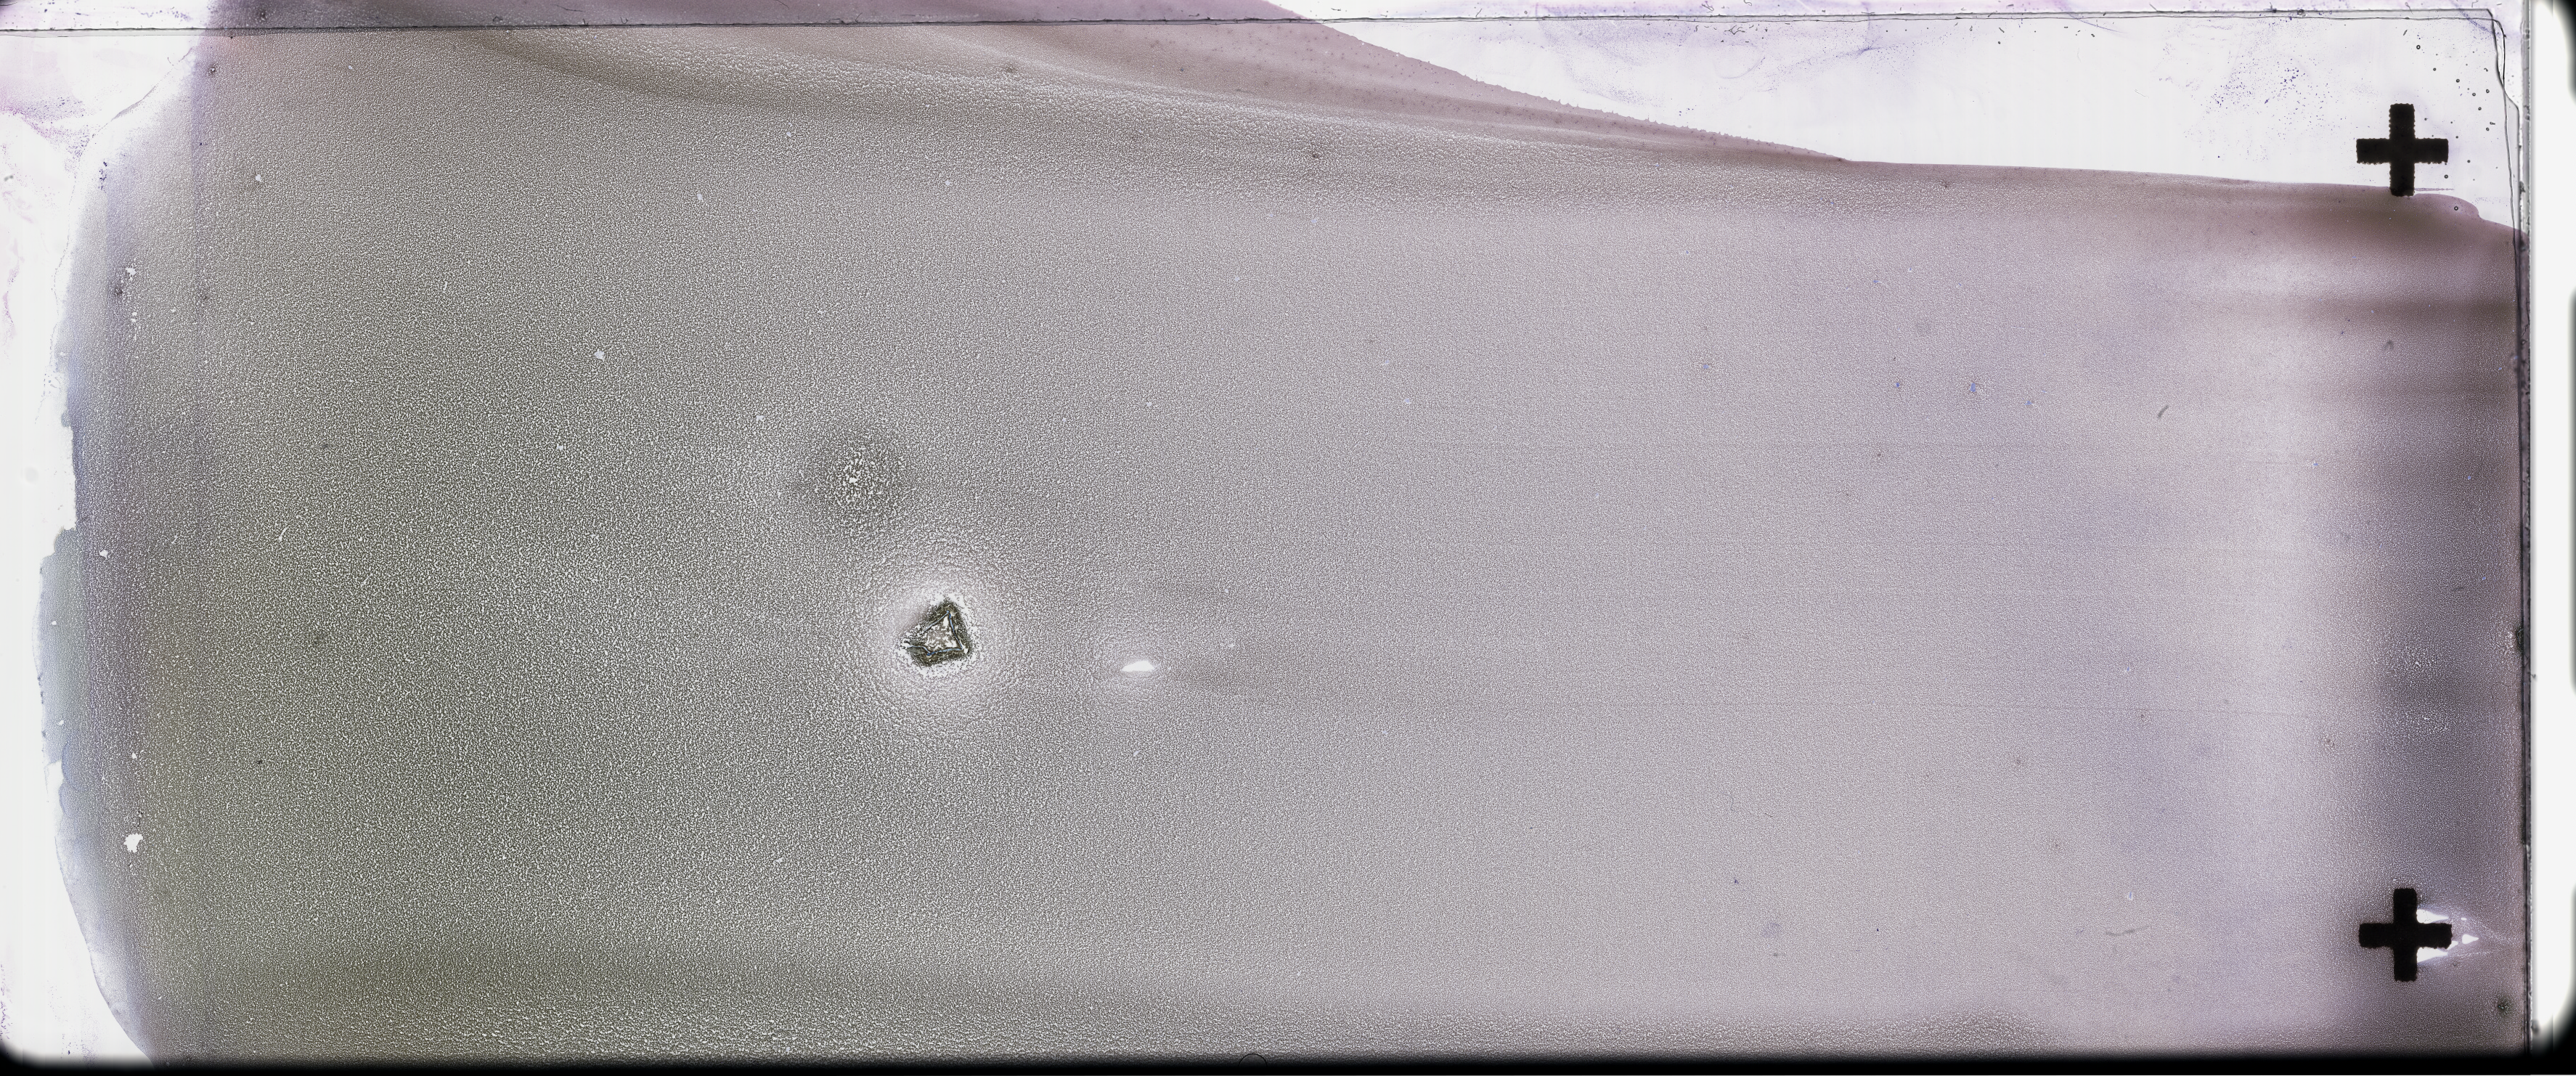
Whole-slide image of a whole blood smear, Wright-Giemsa stain, shown as a low-resolution overview of the whole scanned area (about 57.3 x 23.9 mm), specimen time point: collected on treatment. Female patient.
* from a patient with: Plasma Cell Myeloma